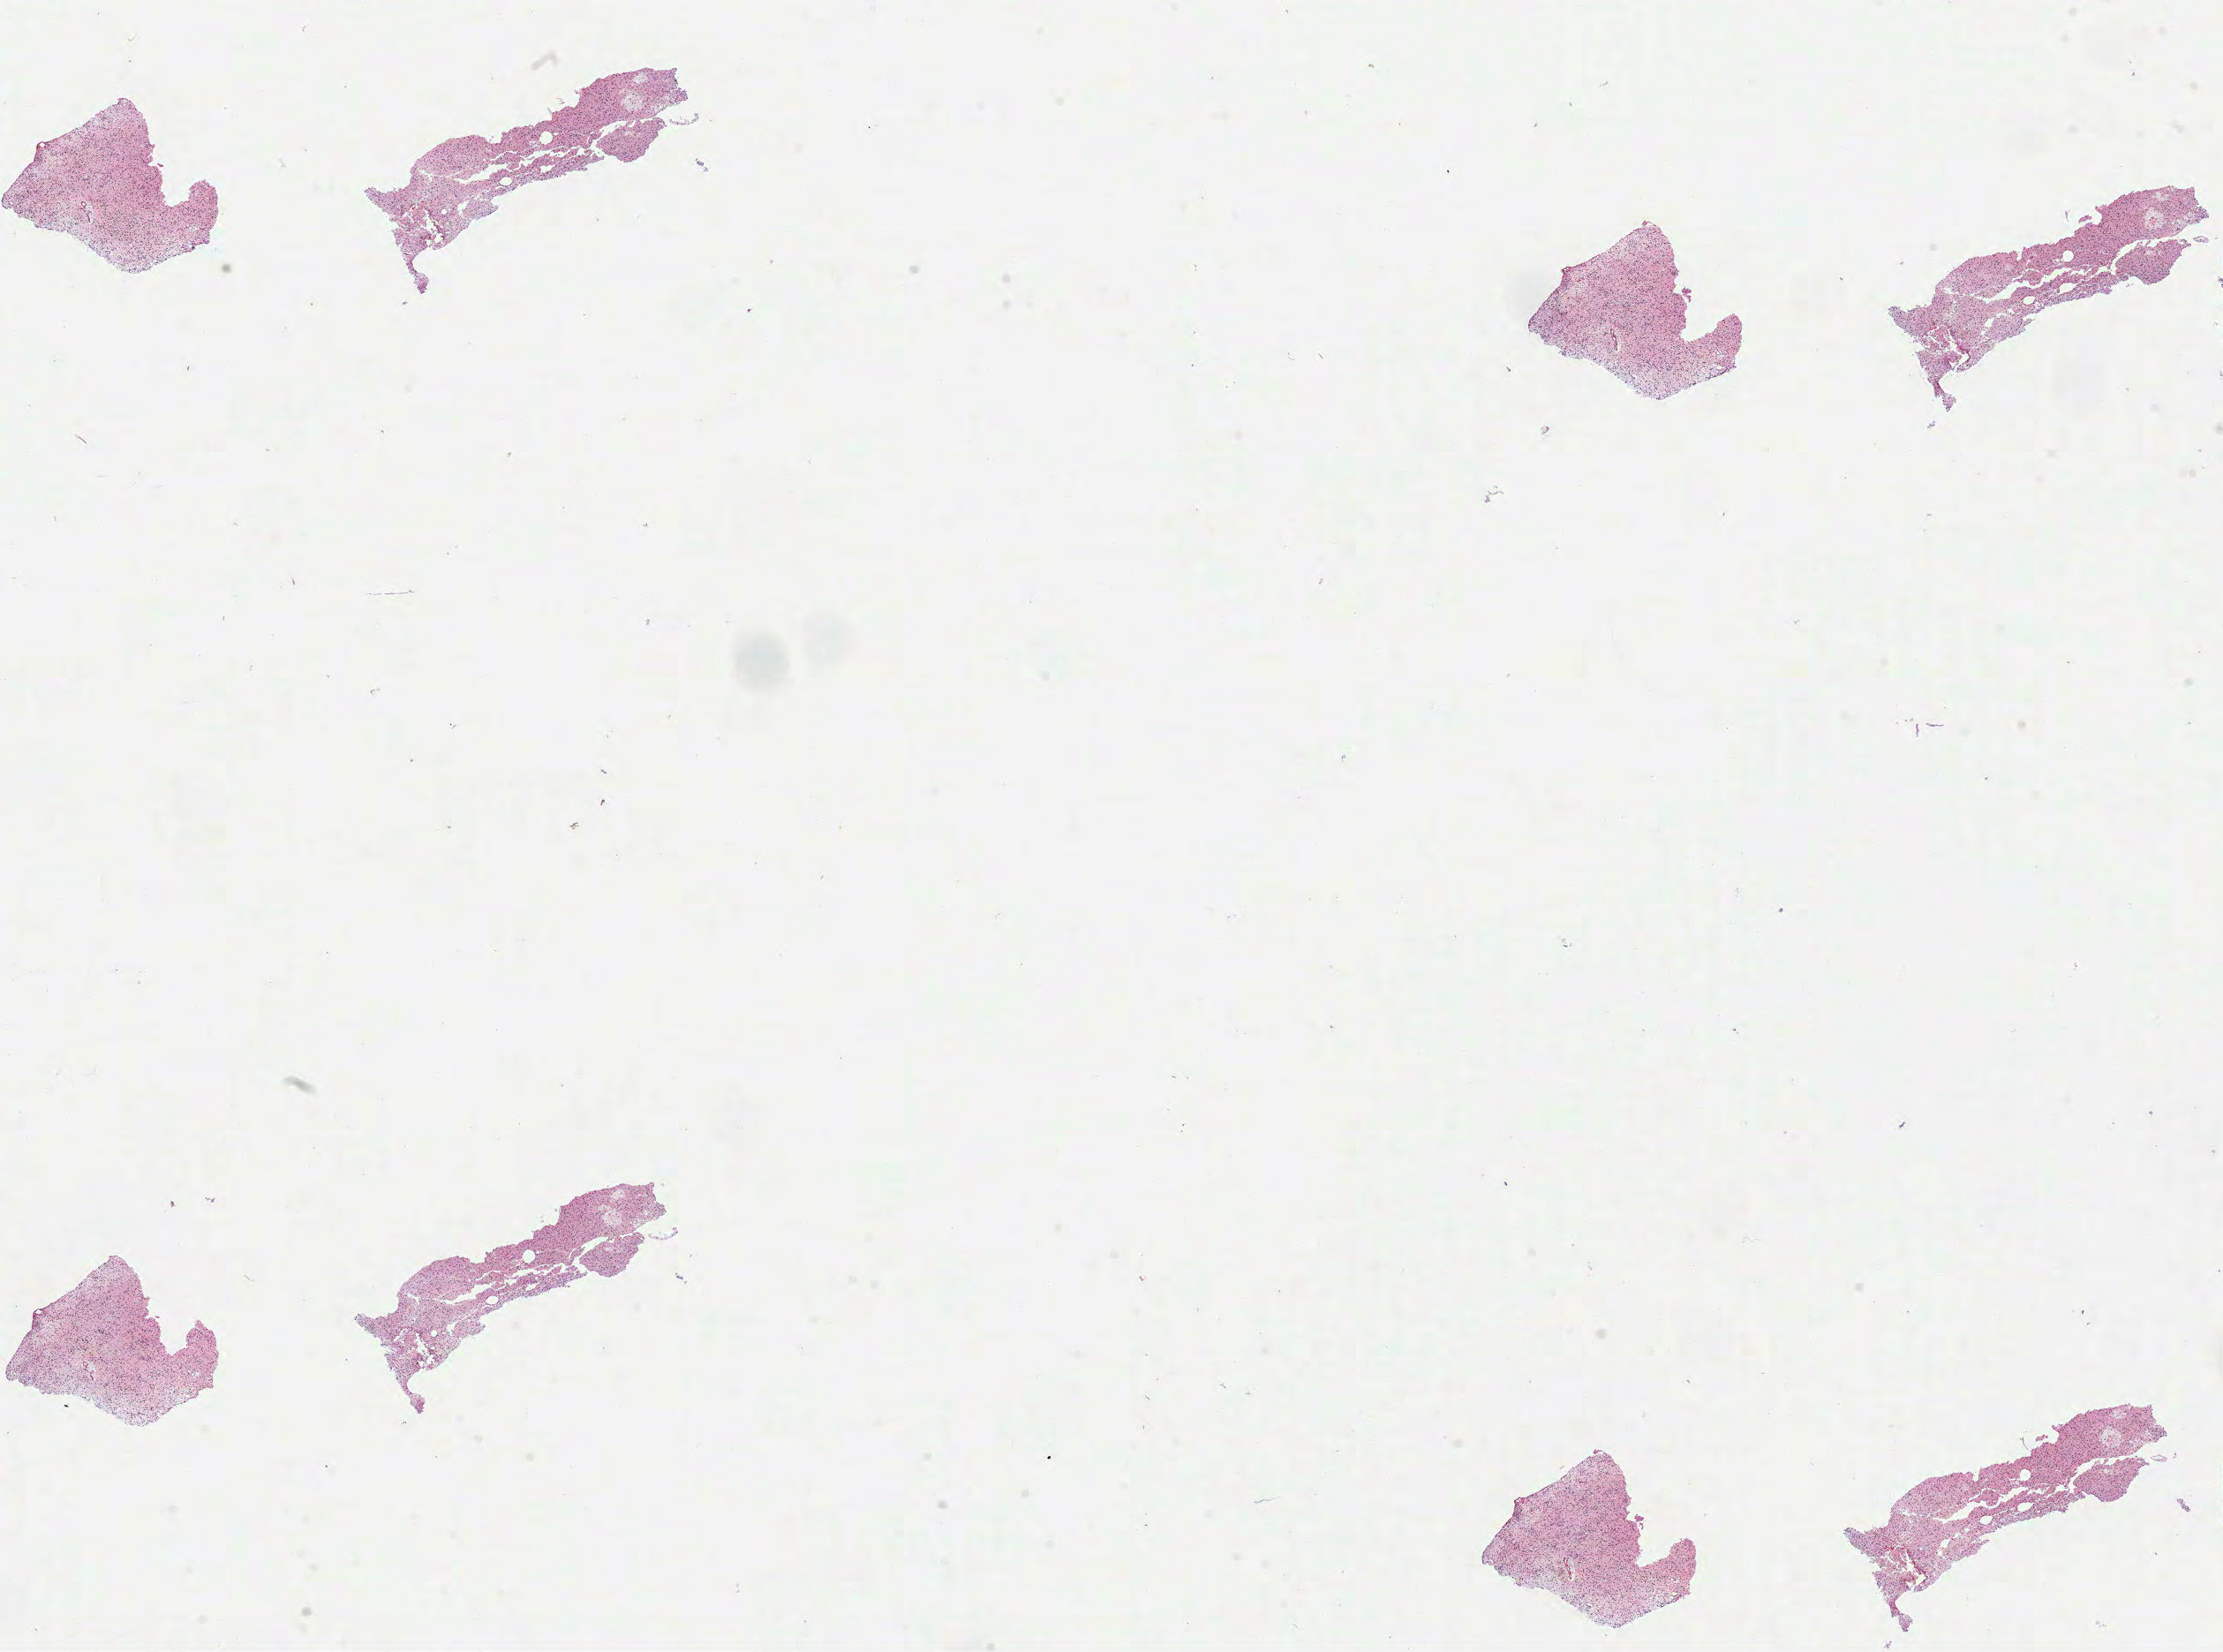
Whole-slide histology image, H&E, low-resolution overview of the scanned area, about 20.3 x 15.1 mm (slide scanned at 40x), formalin-fixed paraffin-embedded (FFPE) diagnostic section, primary tumour sample from the brain. Patient: male, age at initial diagnosis 54 years. Histologic grade: G2 (moderately differentiated).
Diagnosis: Oligodendroglioma, NOS (cerebrum). Laterality: right.